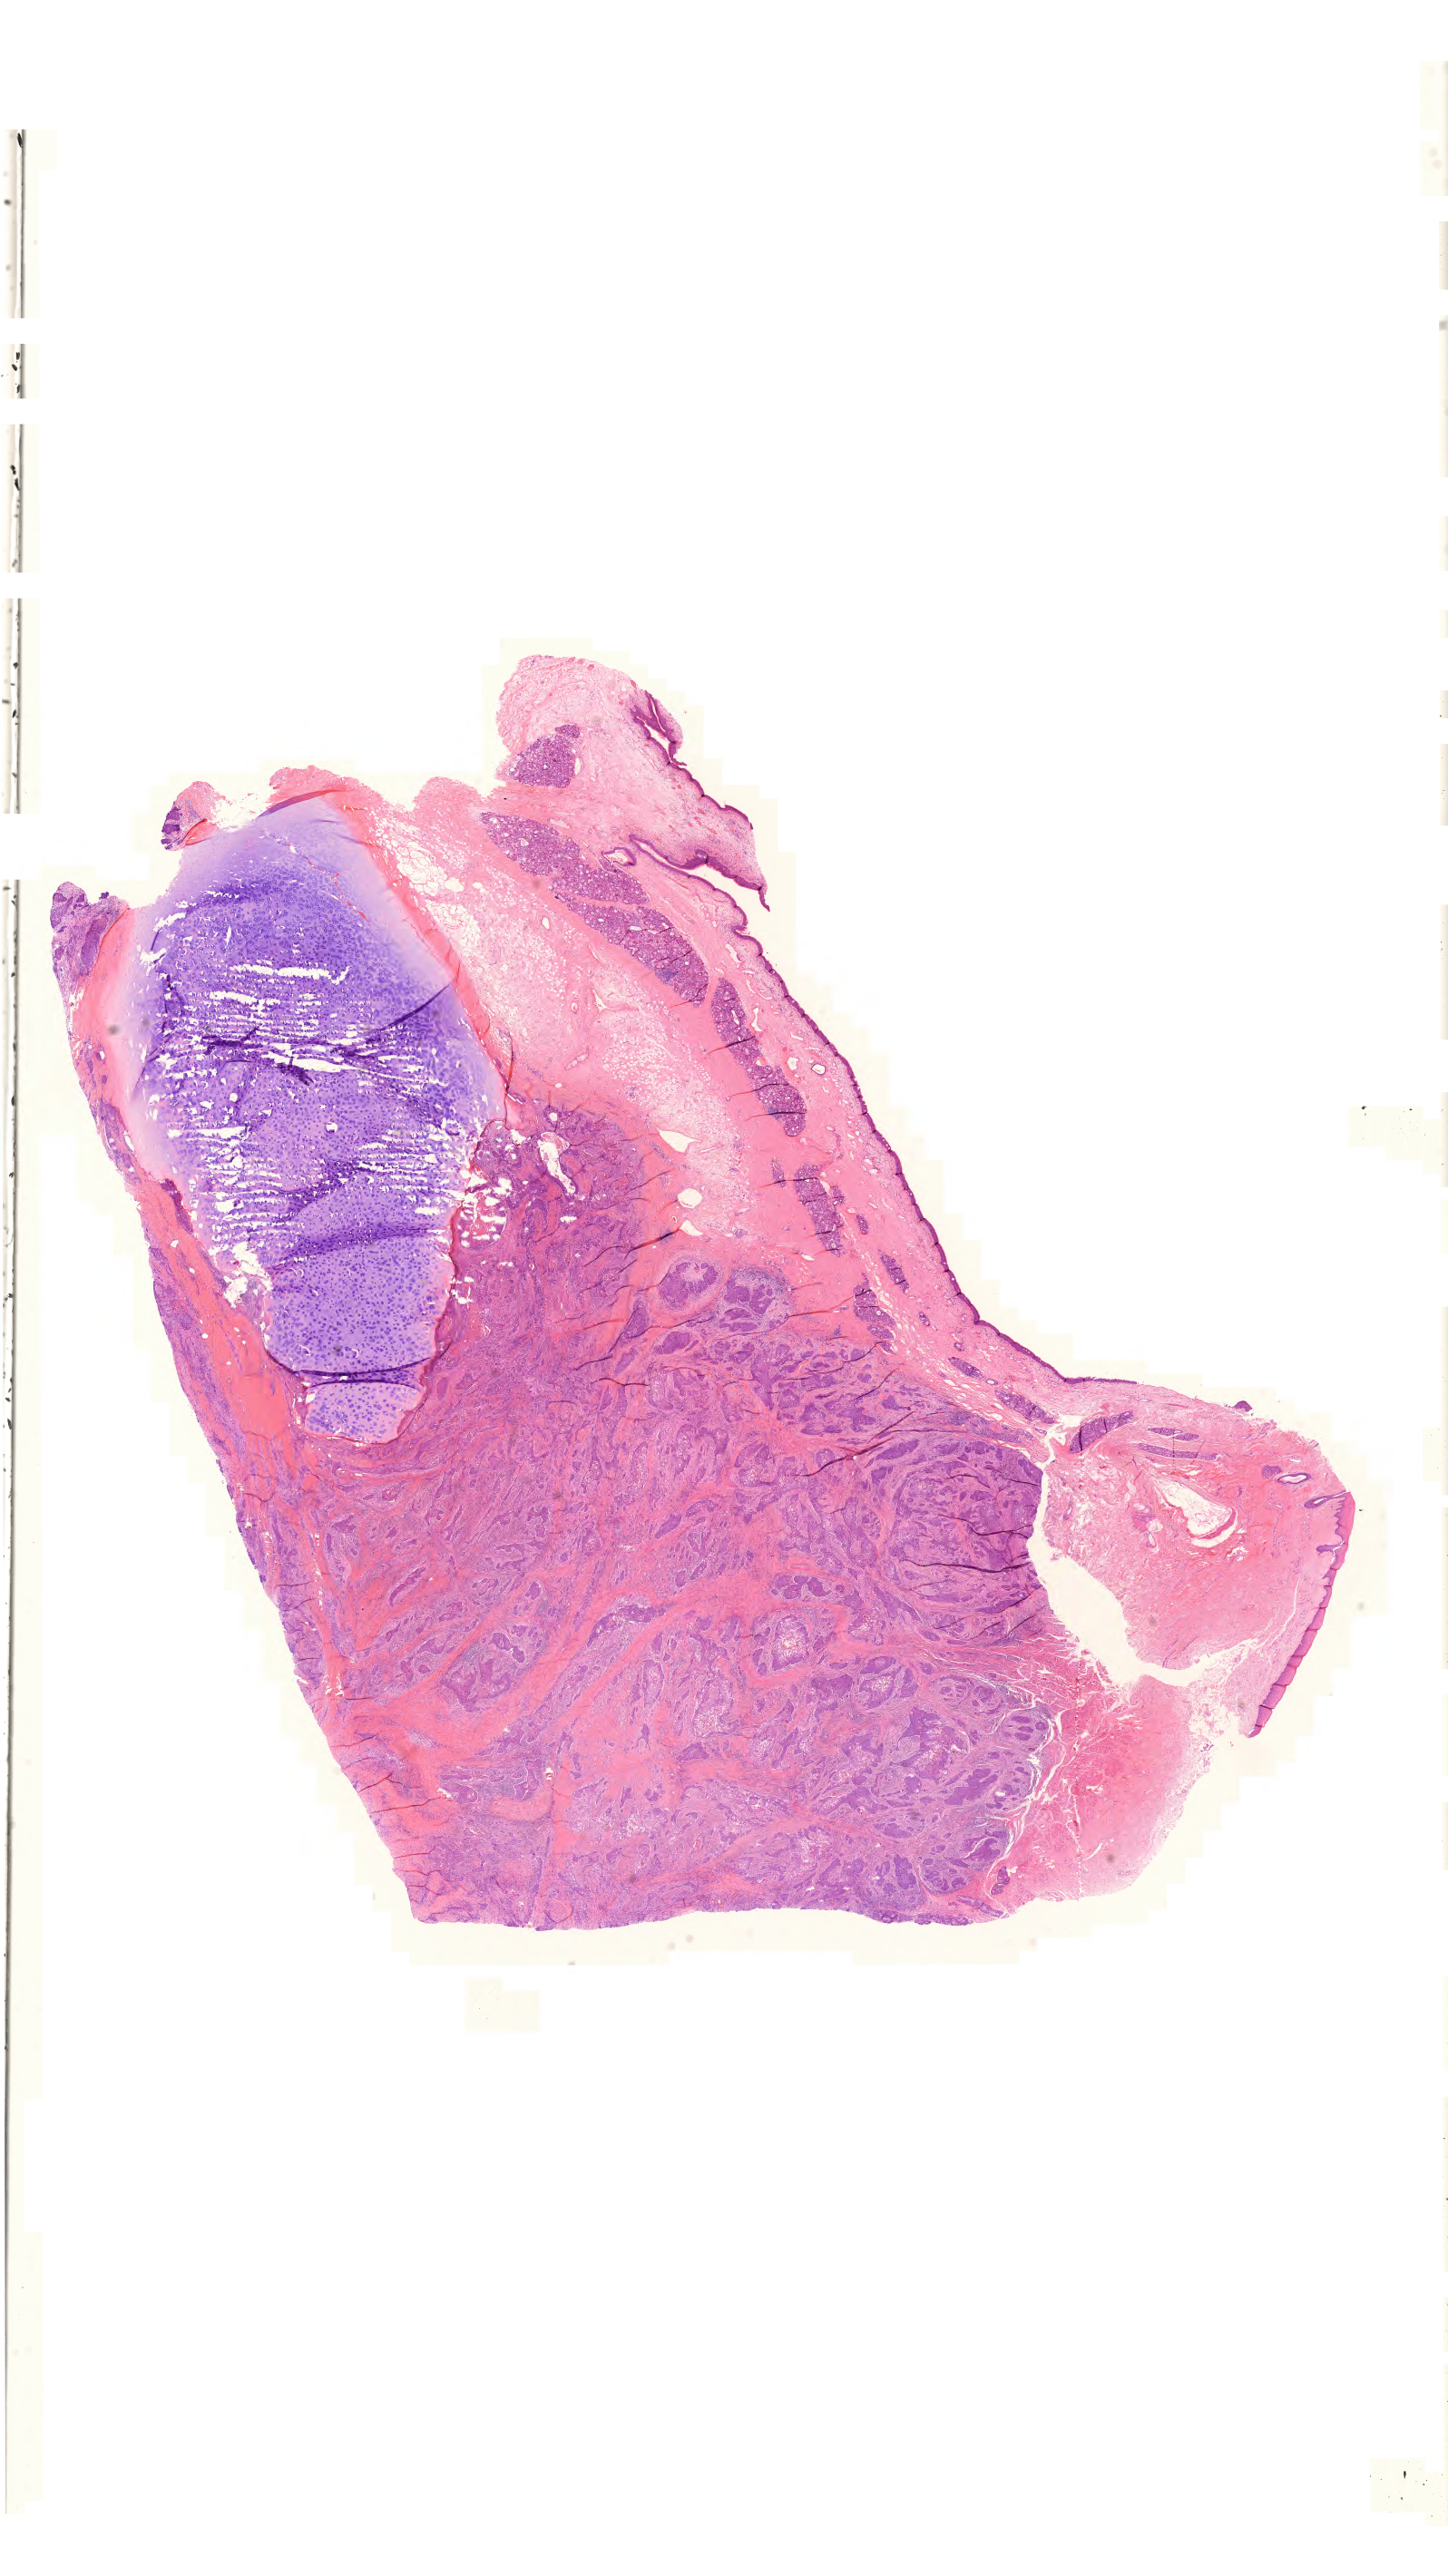
Digitized H&E-stained tissue section (whole slide) — low-resolution overview of the scanned area, about 23.7 x 42.3 mm, FFPE section, head and neck, primary tumour sample. Male, age 52 years at initial diagnosis. Histologic grade: G2 (moderately differentiated).
Pathologic diagnosis: Squamous cell carcinoma, NOS (larynx, NOS). TNM: T4a N2c MX. Laterality: midline. AJCC pathologic stage: IVA (7th edition).